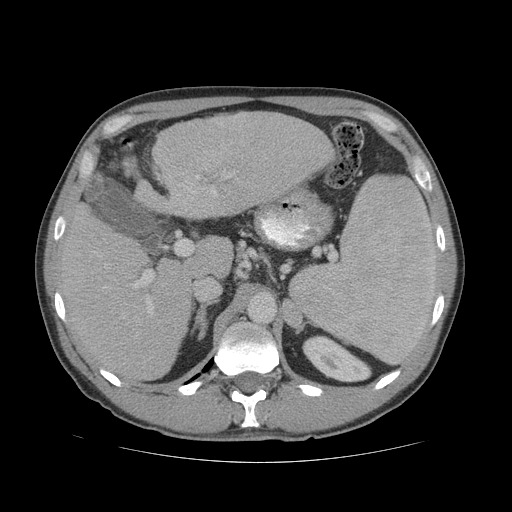
Contrast-enhanced abdominal CT (liver protocol), one axial slice; slice 38 of 81 in the series (ordered by position); reconstruction kernel STANDARD; 140 kVp; soft-tissue window (W 400 / L 40 HU); 512 × 512 image matrix, field of view 400 × 400 mm. Case-level facts recorded for this patient, not image findings: diagnosis: hepatocellular carcinoma (patient treated with transarterial chemoembolisation; whether this scan precedes or follows treatment is not stated here); TNM stage (as recorded): Stage-IVB; Child-Pugh class: B; tumour differentiation: well differentiated.
Structures marked on this image (semi-automatically segmented with operator editing):
- liver parenchyma outside the tumour (the mass and vessels are separate outlines, so this box may not span the whole liver): bounding box <54,112,334,380> (left, top, right, bottom; pixels)
- liver vessels: <133,123,231,314>